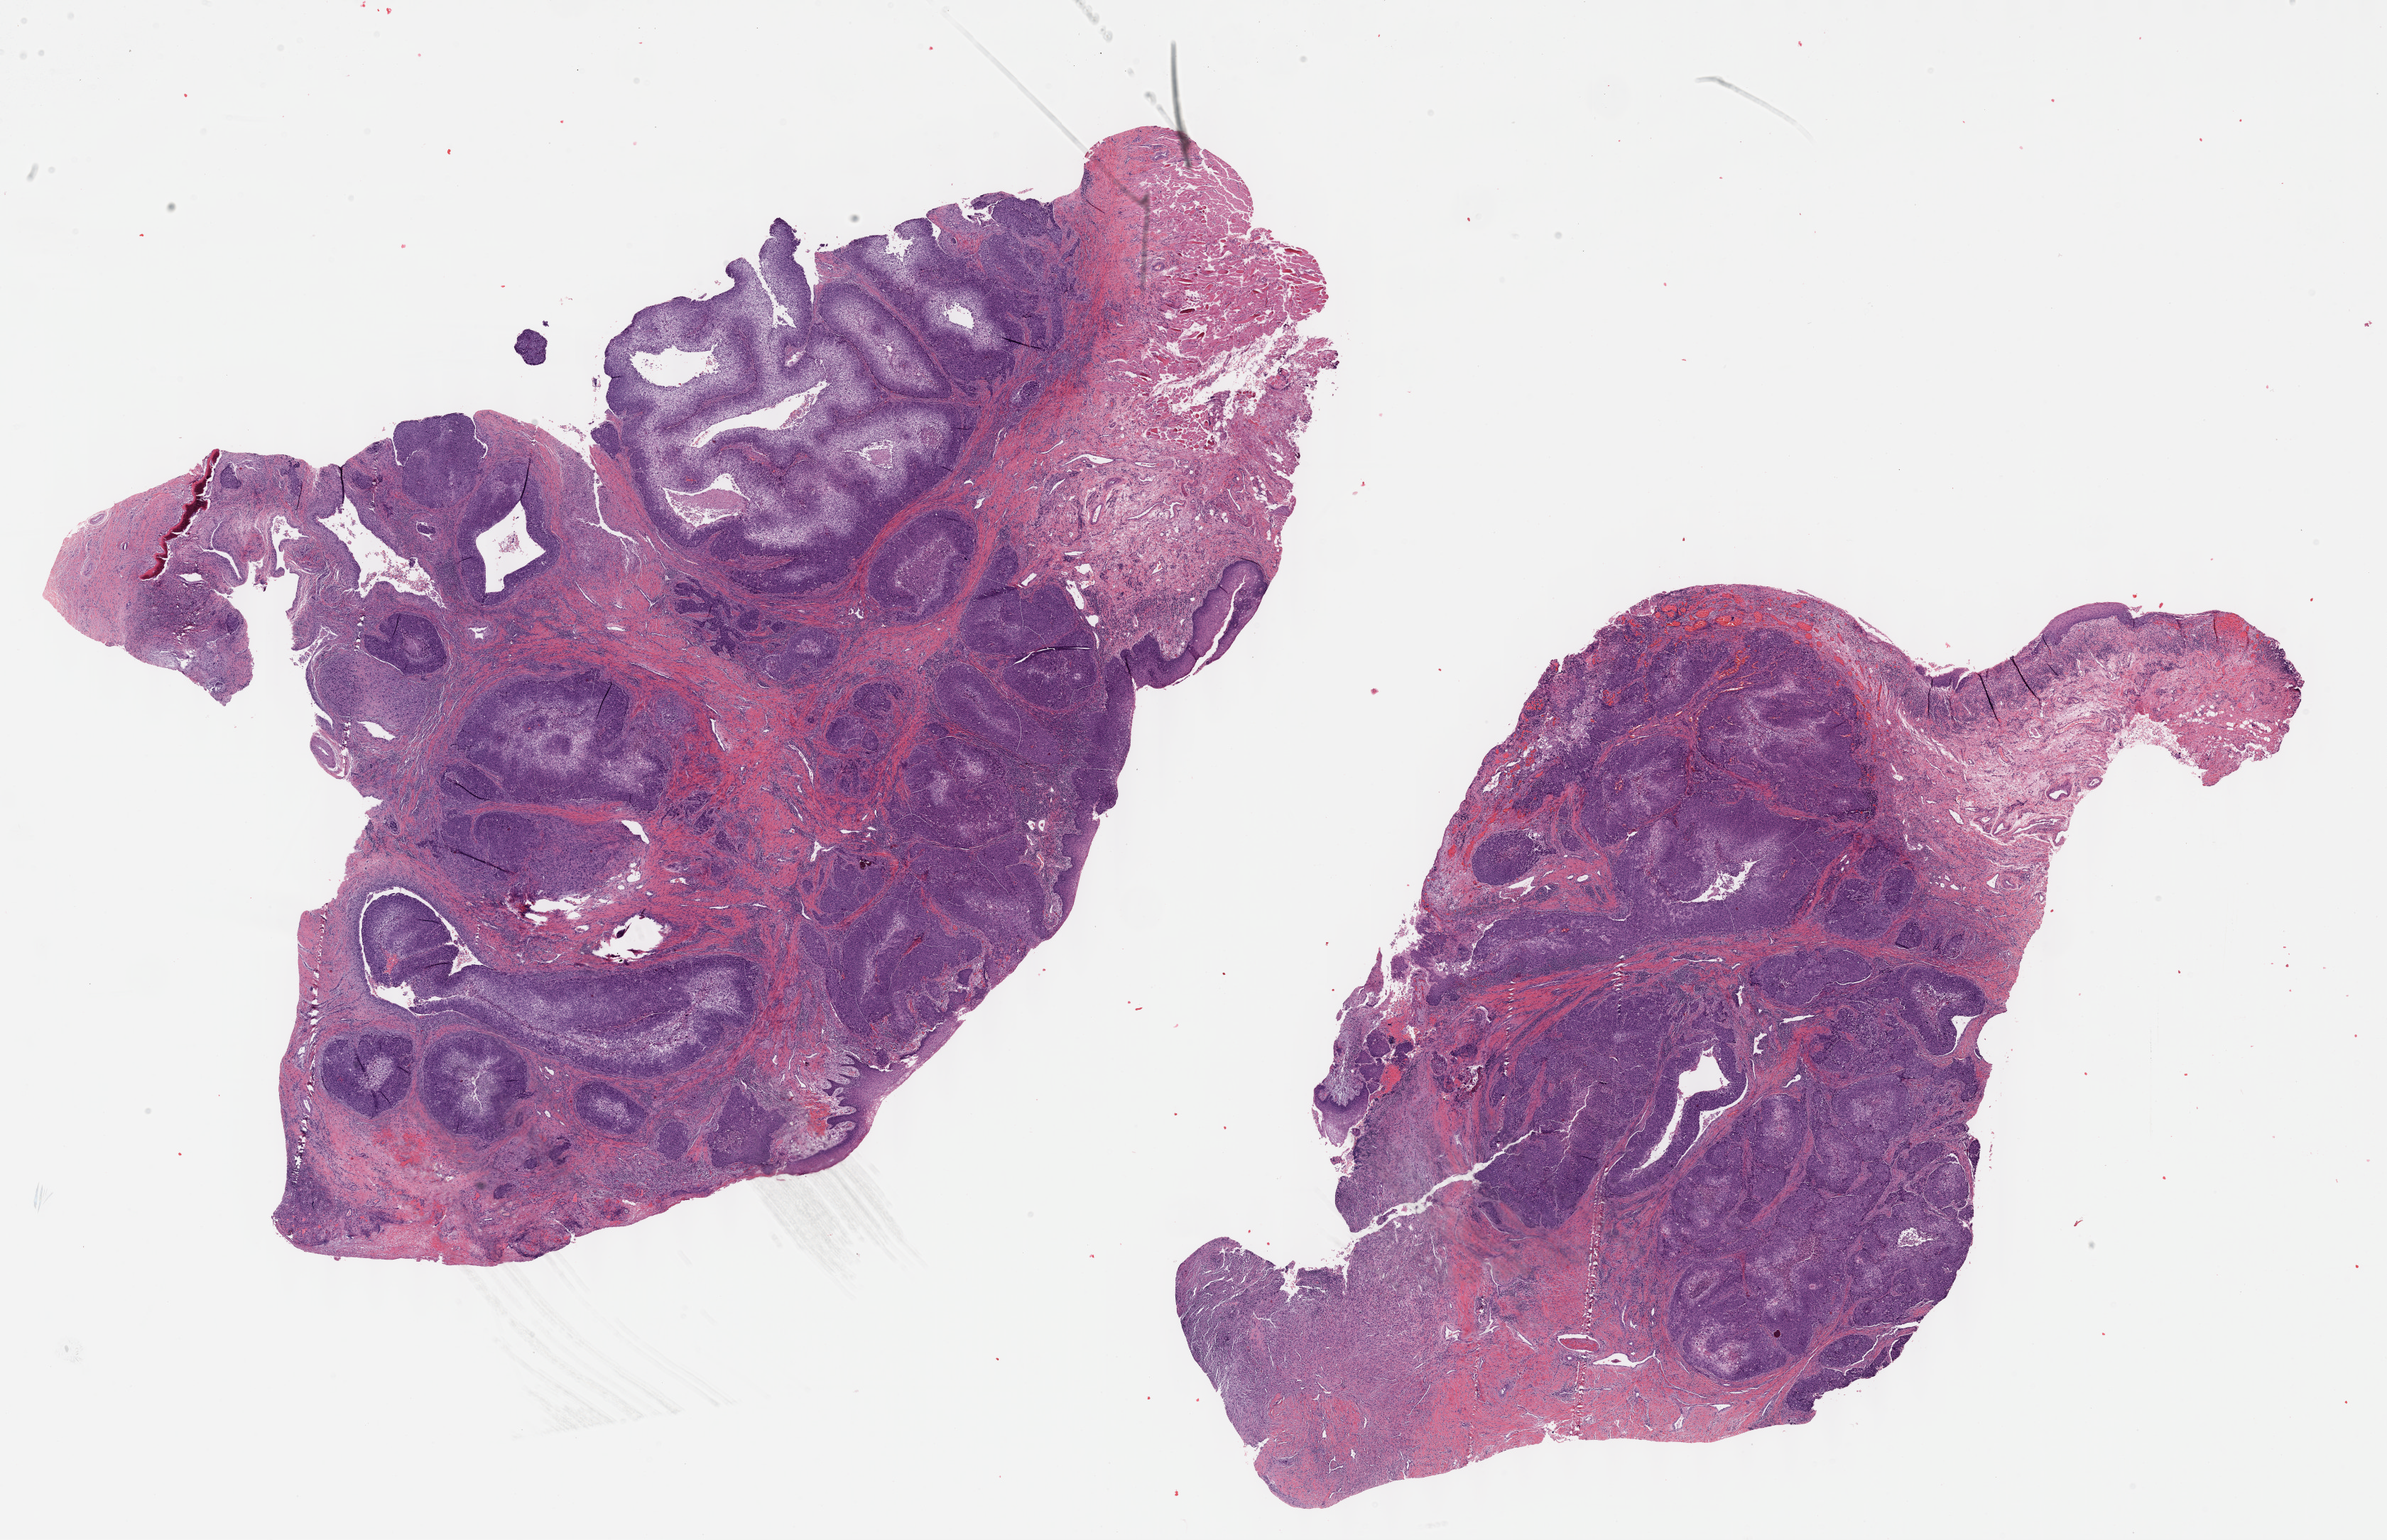
Whole-slide histology image, H&E-stained — a low-resolution overview of the entire scanned area, about 27.2 x 17.5 mm (from a 40x scan); formalin-fixed paraffin-embedded (FFPE) diagnostic section; primary tumour sample from the head and neck. Patient: male, age at initial diagnosis 67 years. Histologic grade: G3 (poorly differentiated).
- histologic diagnosis: Squamous cell carcinoma, NOS (floor of mouth, NOS)
- TNM: T2 N0
- AJCC pathologic stage: II (7th edition)